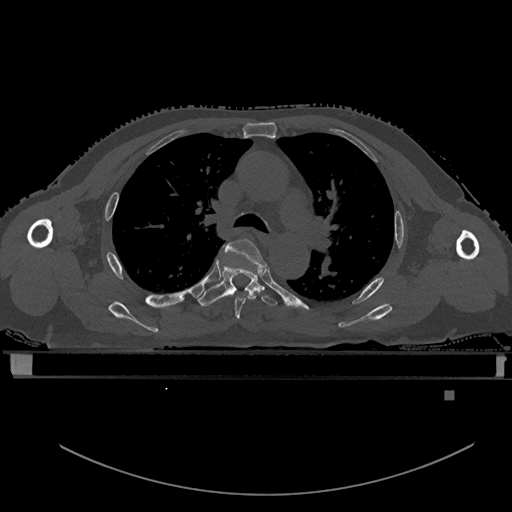
CT including the spine, one axial slice. Bone window (W 1800 / L 400 HU). 0.5 mm slice thickness. 512 × 512 image matrix, field of view 456 × 456 mm. Male patient, age 82 years. Case-level facts recorded for this patient, not image findings: primary cancer: prostate; vertebrae with lytic lesions (as recorded): T11, T9, T8, T2.
Structures marked on this image (semi-automatically segmented with operator editing):
- T4 vertebra: box from (x=222, y=238) to (x=267, y=319) px
- T5 vertebra: (x=198, y=255)–(x=278, y=307)